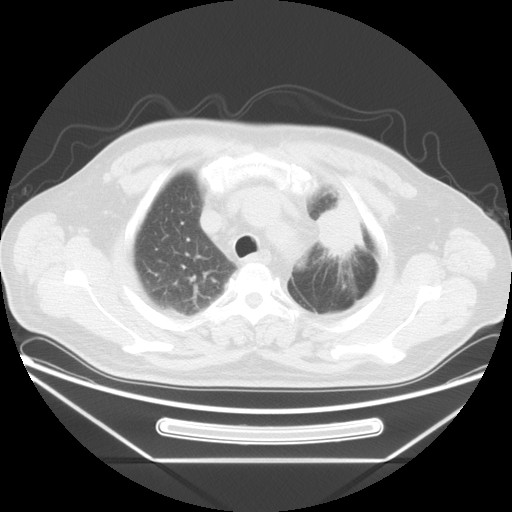
Chest CT, one axial slice; position 32 of 38 along the scan axis; 120 kVp; lung window (W 1500 / L -600 HU); 512 × 512 image matrix, field of view 411 × 411 mm. Patient: male, 61 years. From the clinical record (not read from this slice): clinical TNM (as recorded): T2a N0 M0; histopathological grade: G3.
Annotated regions visible in this slice (rectangle marked by the reading radiologist):
- lung tumour (recorded histology: small cell carcinoma): bounding box (x1, y1, x2, y2) in pixels: (304, 198, 372, 271)